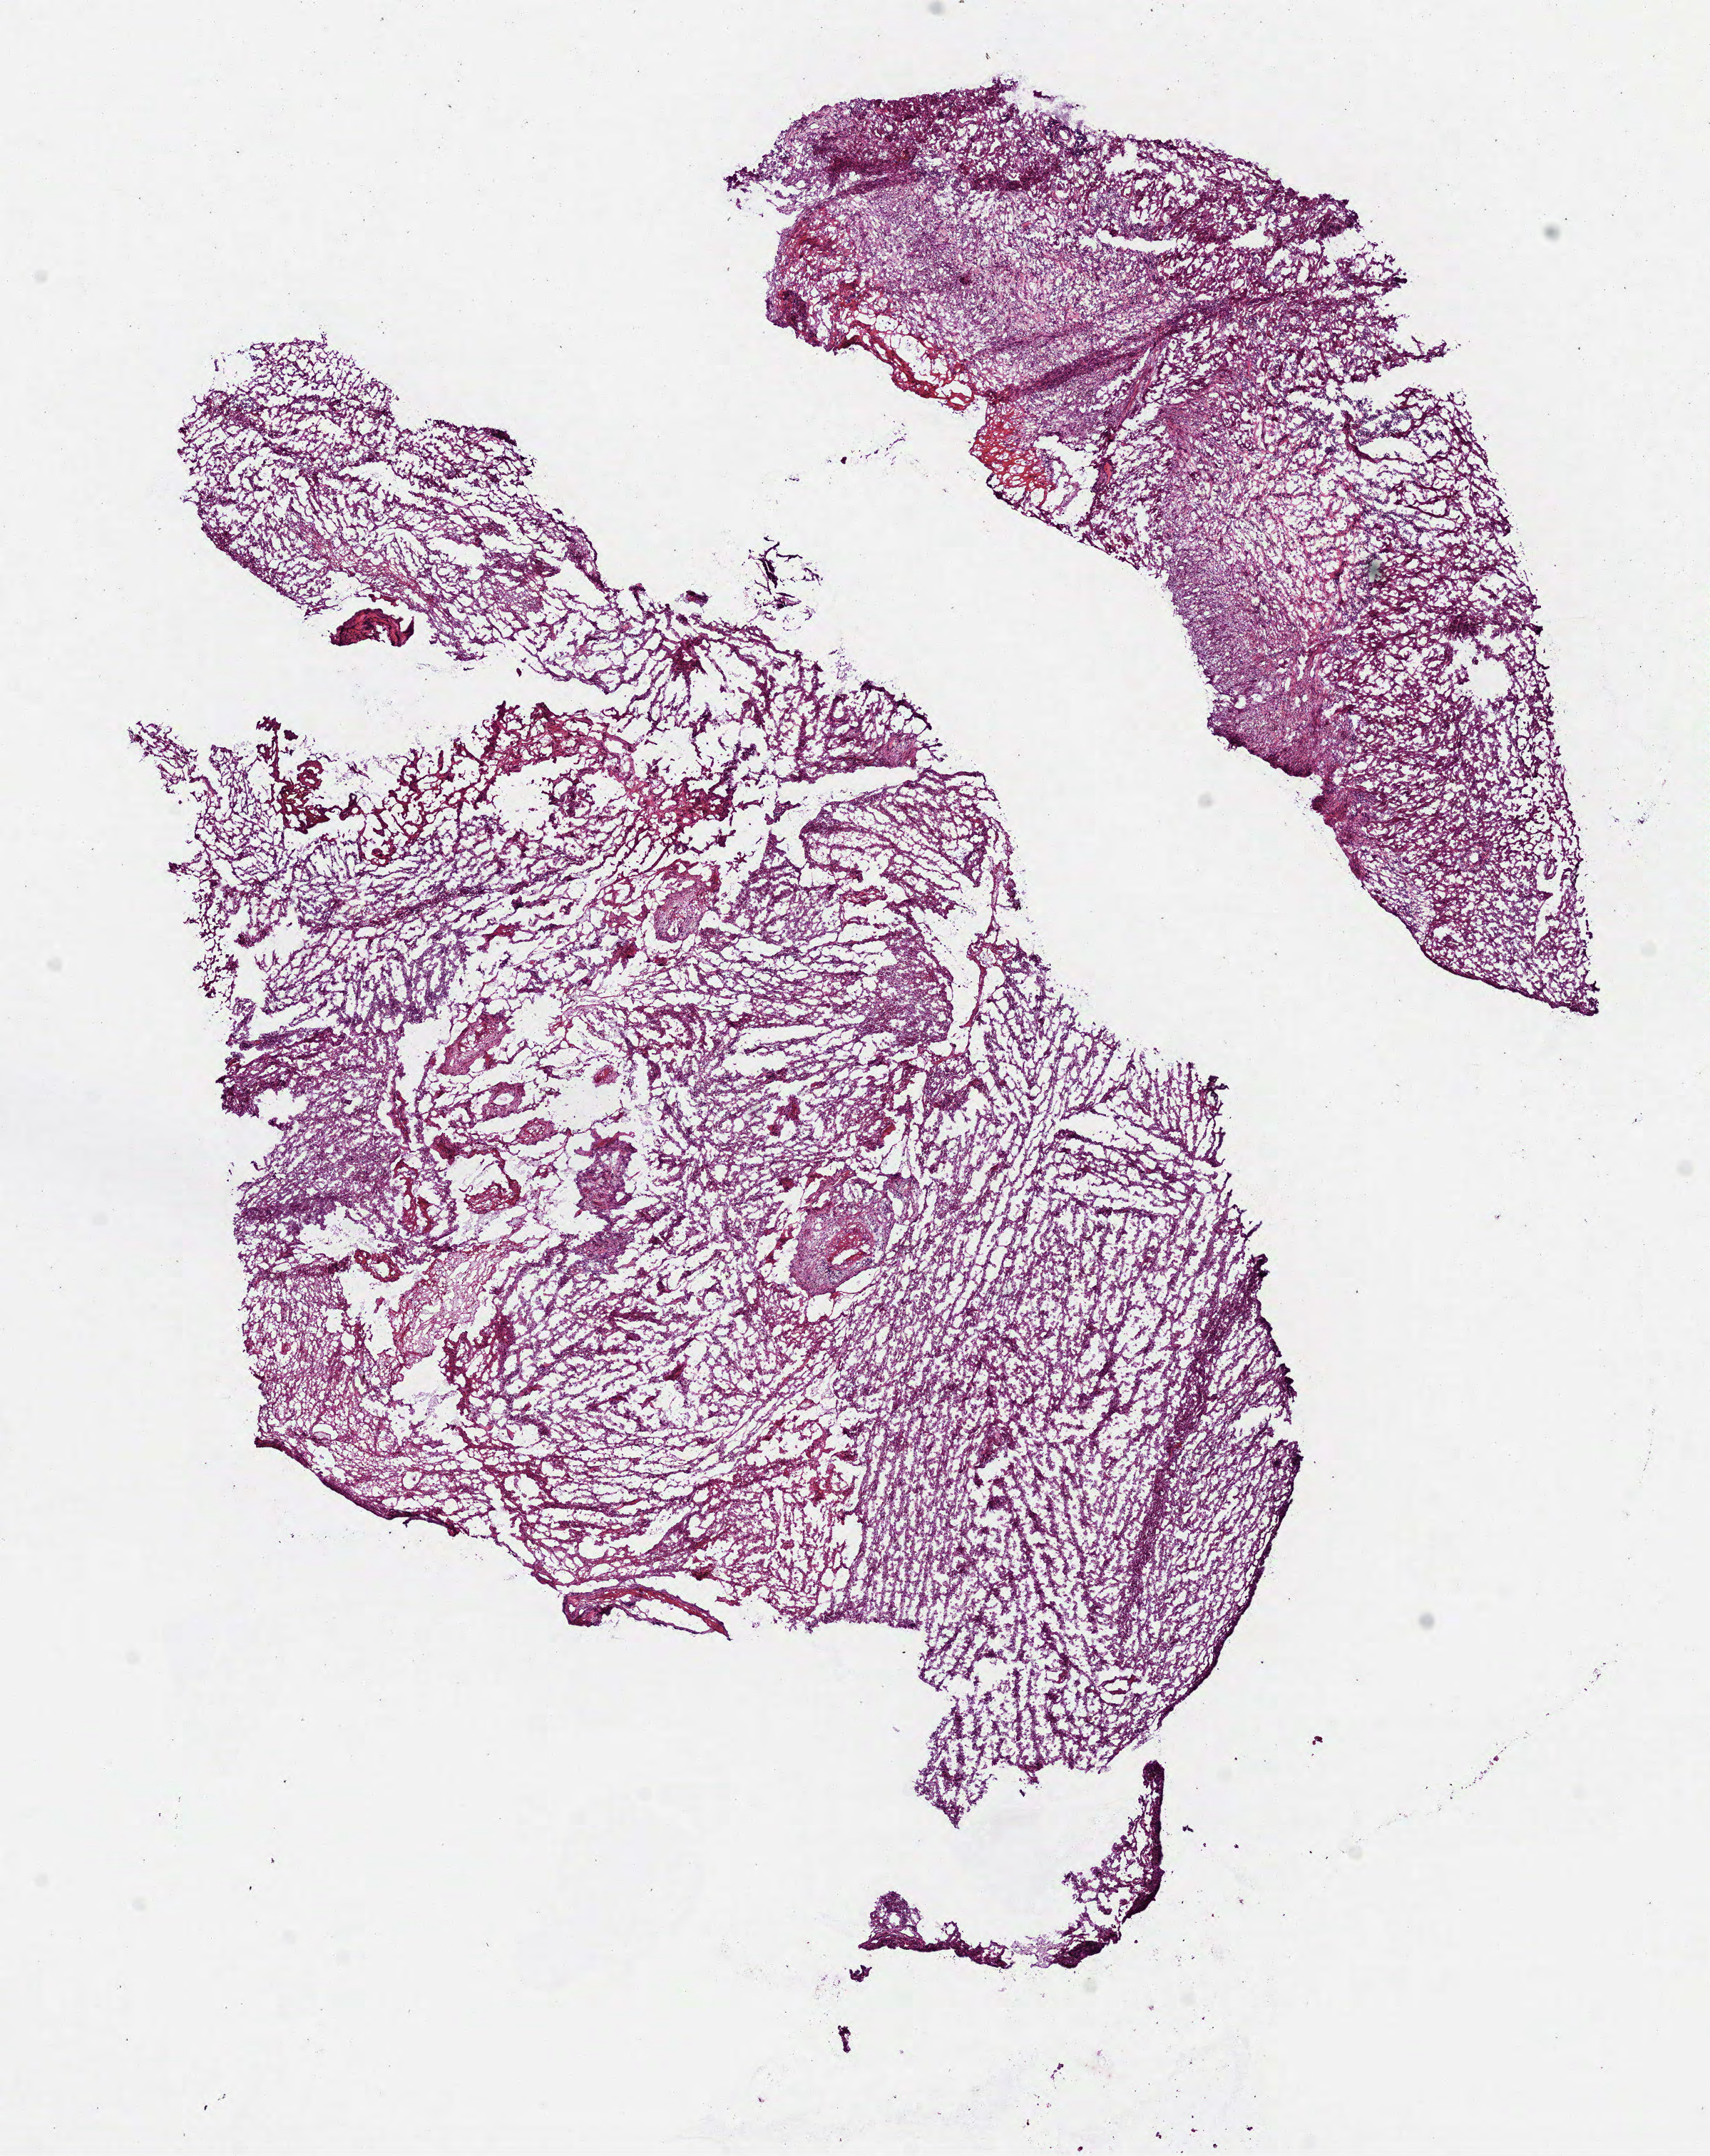
Digitized H&E-stained tissue section (whole slide) — shown as a low-resolution overview of the whole scanned area (about 9.7 x 12.2 mm, from a 40x scan); frozen section from the bottom of the tissue portion; brain, primary tumour sample. Patient: male, age at initial diagnosis 63 years. Composition of this section per pathologist review: tumour cells 100%, tumour nuclei 80%, normal cells 0%, stromal cells 0%, necrosis 0%.
* diagnosis: Glioblastoma